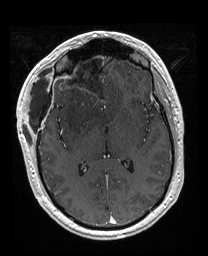
Brain MRI from a brain-tumour surgery series, one axial slice. Slice 95 of 176 in the series (ordered by position). T1-weighted post-contrast. 1 mm slice thickness. 208 × 256 image matrix, field of view 208 × 256 mm. Case-level facts recorded for this patient, not image findings: histopathology: Astrocytoma; WHO grade: 4; IDH mutation: yes.
Outlined on this slice (manually delineated by an expert):
- previous resection cavity: bounding box (x1, y1, x2, y2) in pixels: (56, 52, 106, 111)